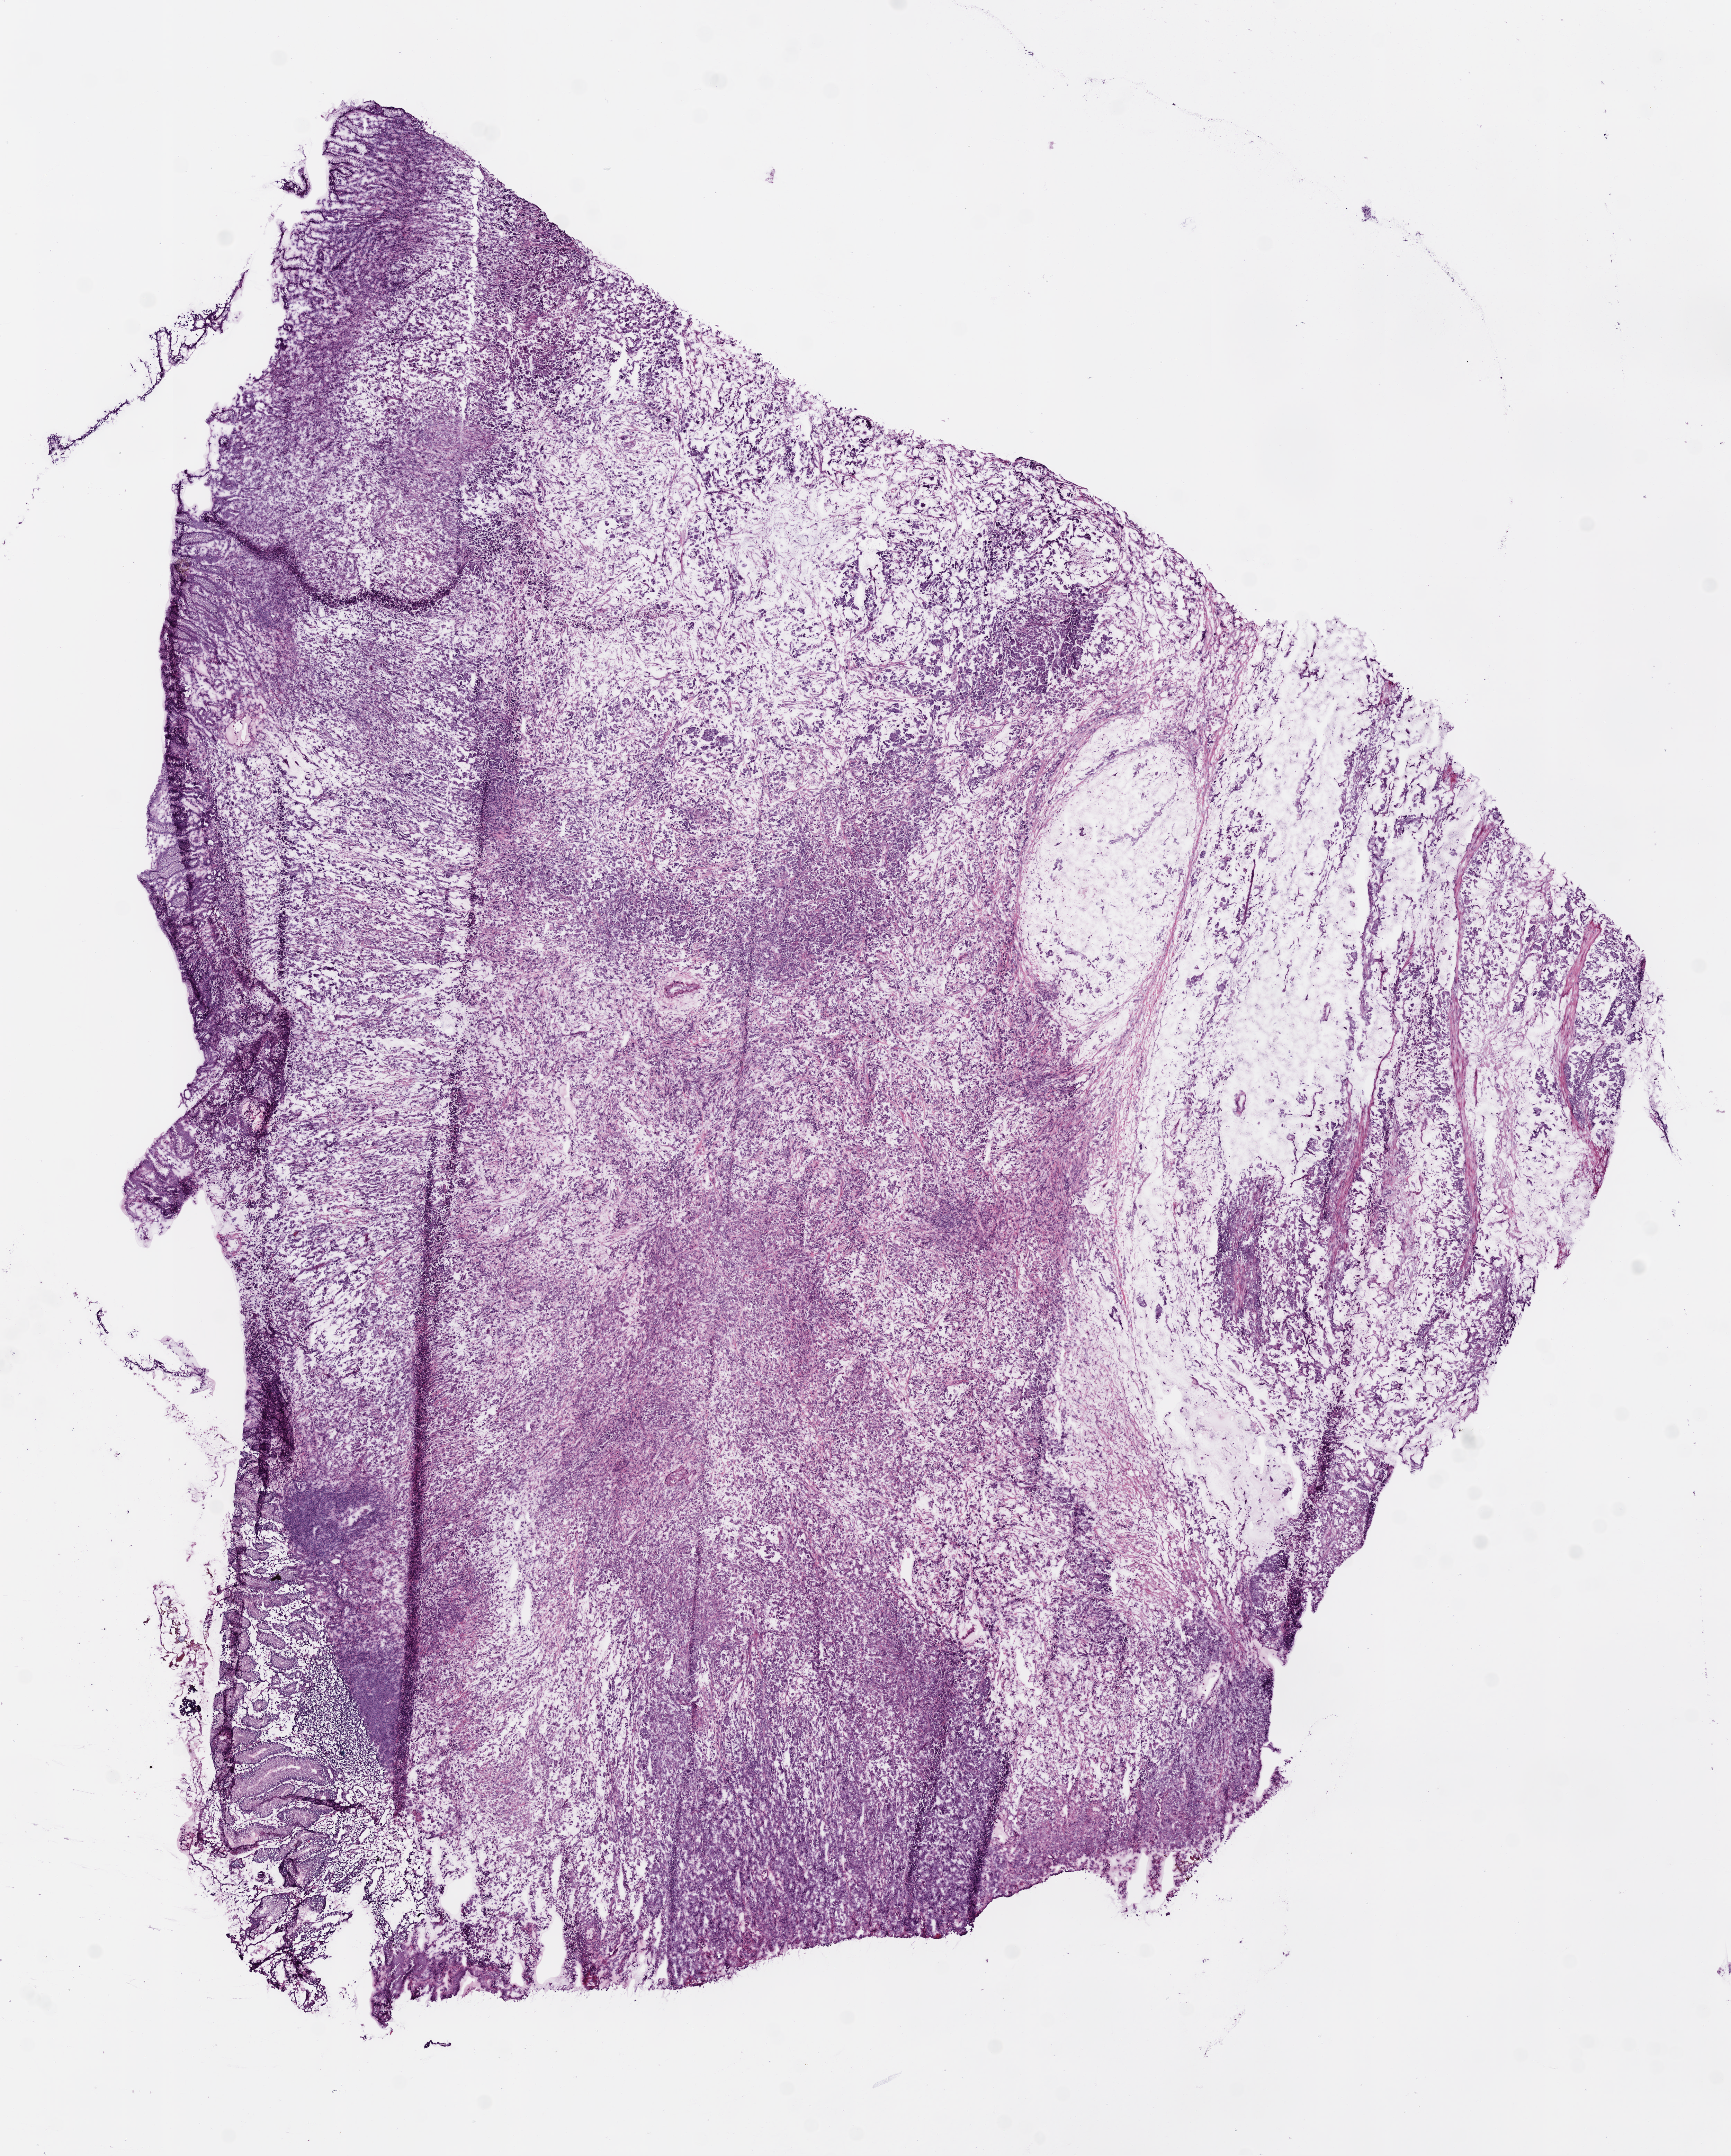
Whole-slide histology image, H&E, low-resolution overview of the scanned area, about 10.0 x 12.5 mm; frozen section; stomach, primary tumour sample. Female patient; age at initial diagnosis 67 years. Histologic grade: G3 (poorly differentiated). Composition of this section per pathologist review: tumour cells 80%, tumour nuclei 70%, normal cells 10%, stromal cells 10%, necrosis 0%.
Pathologic diagnosis: Carcinoma, diffuse type. TNM: T4a N2 M1. Lymph nodes positive (case pathology): 6 of 39 examined. AJCC pathologic stage: IV (7th edition).